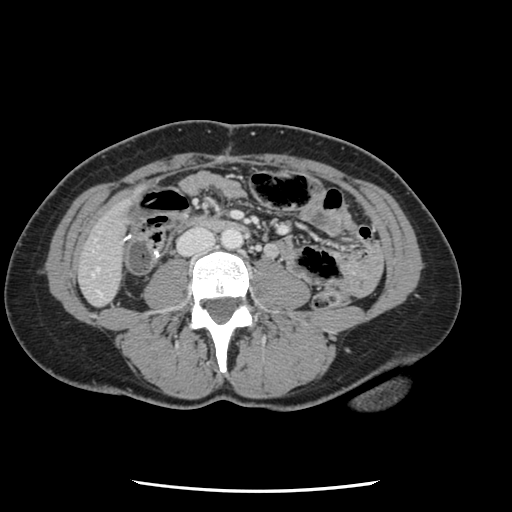
Contrast-enhanced abdominal CT, one axial slice. 120 kVp. Intravenous contrast given. Soft-tissue window (W 400 / L 40 HU). 2.5 mm slice thickness. 512 × 512 image matrix, field of view 330 × 330 mm. Female patient, age 43 years. Case-level facts recorded for this patient, not image findings: diagnosis: colorectal cancer liver metastases, imaged before liver resection.
Outlined on this slice (manually delineated by an expert):
- liver: bounding box <80,203,128,305> (left, top, right, bottom; pixels)
- planned liver remnant (the part of the liver to remain after resection): <80,202,129,305>